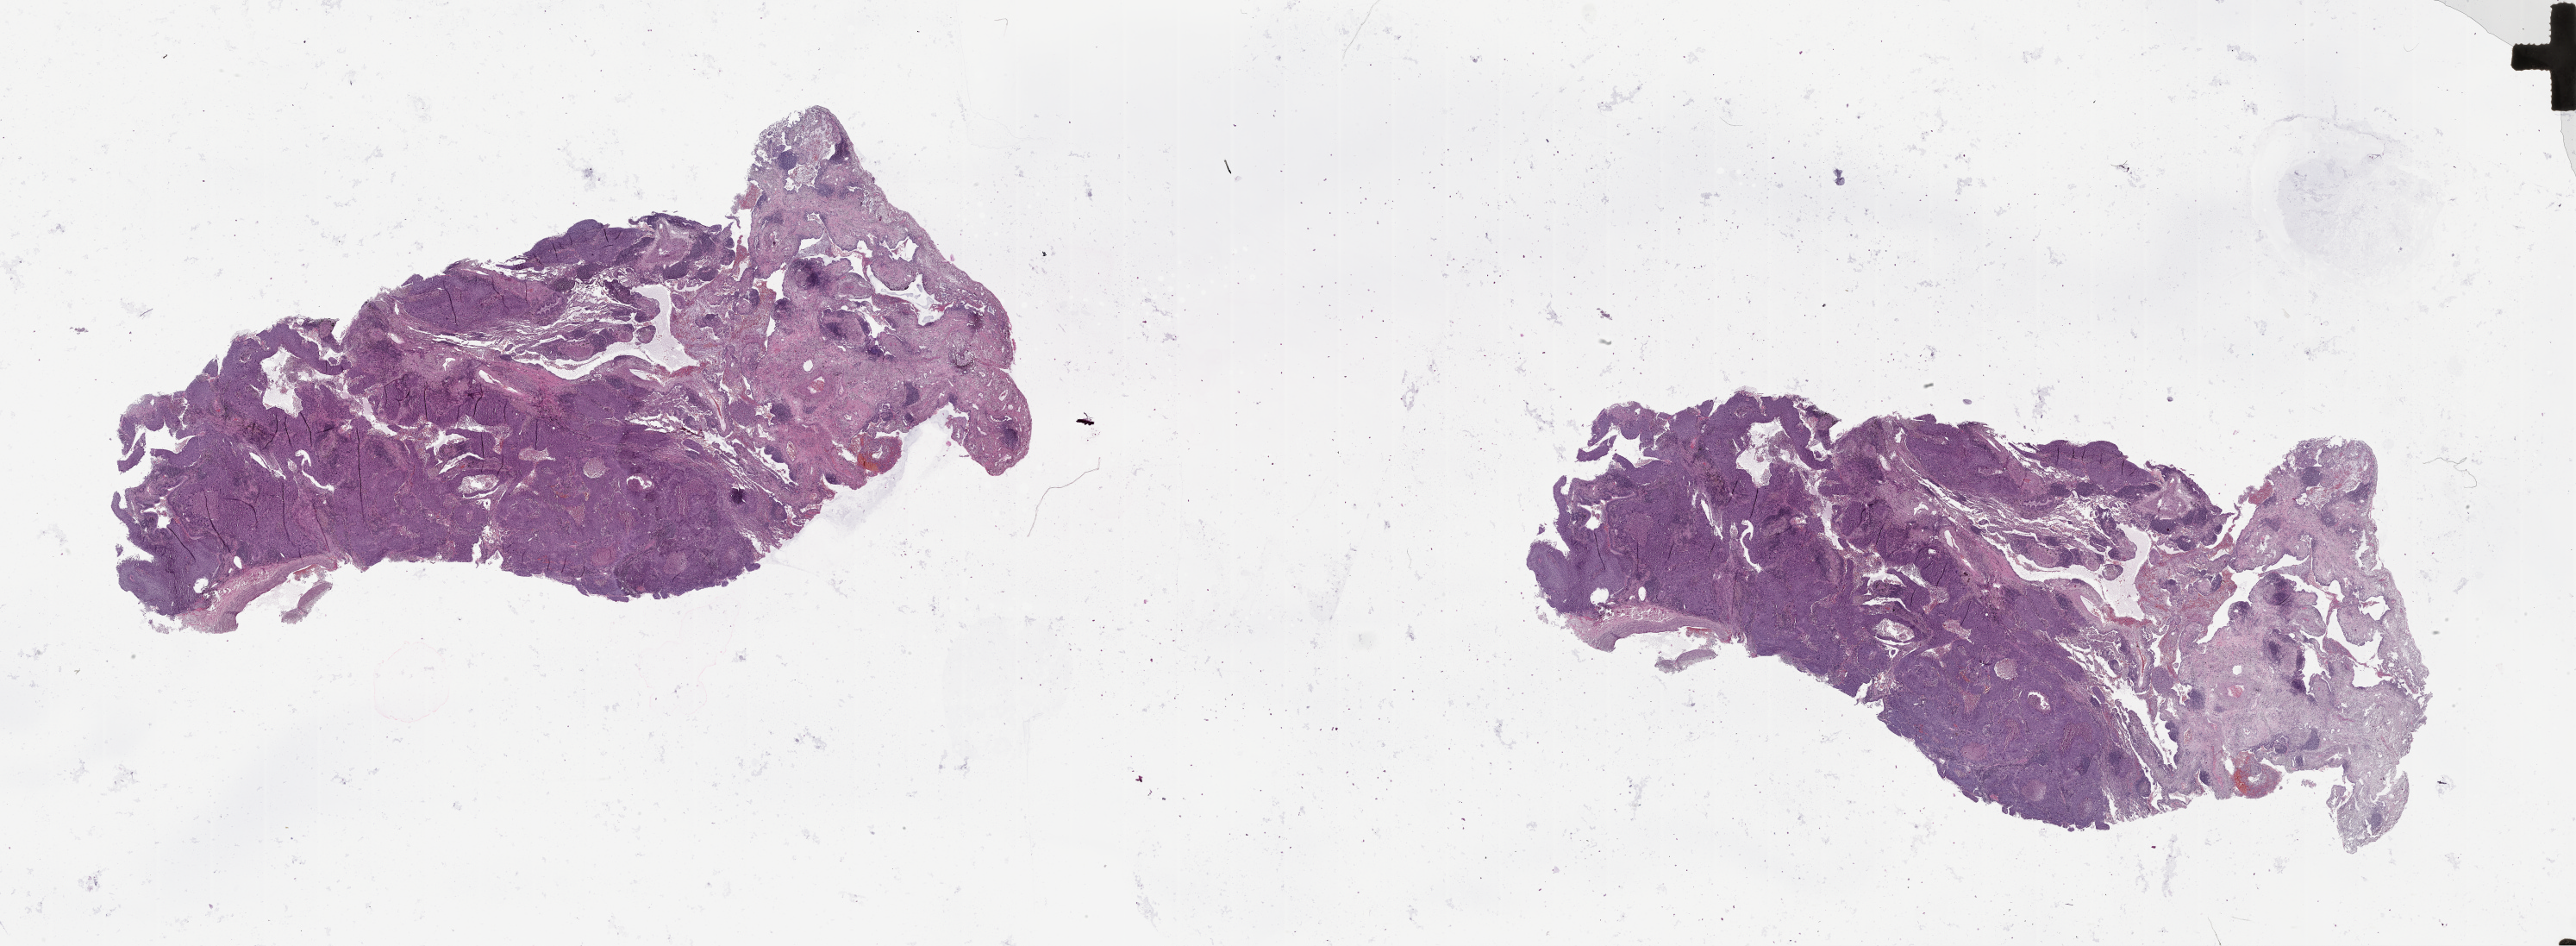
Whole-slide histology image, Hematoxylin and eosin (H&E) stained — a low-resolution overview of the entire scanned area, about 48.1 x 17.7 mm (acquisition: 20x scan); tumour tissue sample, lung. 75-year-old male patient.
Patient diagnosis (cohort enrolment): squamous cell carcinoma (lung).